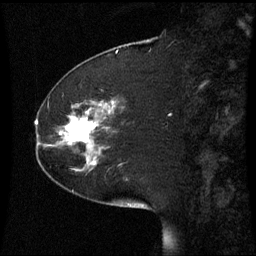
Breast MRI (dynamic contrast-enhanced), one sagittal slice. Slice 19 of 60 in the series (ordered by position). Dynamic contrast-enhanced series, image 2 of 3 at this slice position (ordered by acquisition). 1.5 T. TE 4.2 ms, TR 8.9 ms. 2.2 mm slice thickness. 256 × 256 image matrix, field of view 220 × 220 mm. Female patient, age 51 years. Case-level facts recorded for this patient, not image findings: setting: breast cancer imaged before/during neoadjuvant chemotherapy; receptor status: HR-positive, HER2-negative.
Structures marked on this image (semi-automatic segmentation, software-assisted and operator-edited):
- analysis volume of interest (the breast-tissue region the enhancement analysis was run in; not a lesion): box from (x=44, y=102) to (x=109, y=169) px
- tumour enhancement mask (voxels above the 70 % enhancement threshold inside the analysis volume of interest): (x=60, y=118)–(x=95, y=143)